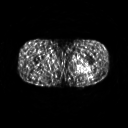
FDG PET of an extremity soft-tissue mass (from a PET/CT study), one axial slice; slice 240 of 267 in the series (ordered by position); 3.27 mm slice thickness; 128 × 128 image matrix. Patient: male, 27 years. Case-level facts recorded for this patient, not image findings: histological type: extraskeletal osteosarcoma; grade: high; site of the primary tumour: left adductur.
Structures marked on this image (expert contour drawn on MRI and transferred to this co-registered scan by the dataset authors):
- gross tumour volume (mass): box from (x=70, y=61) to (x=95, y=75) px